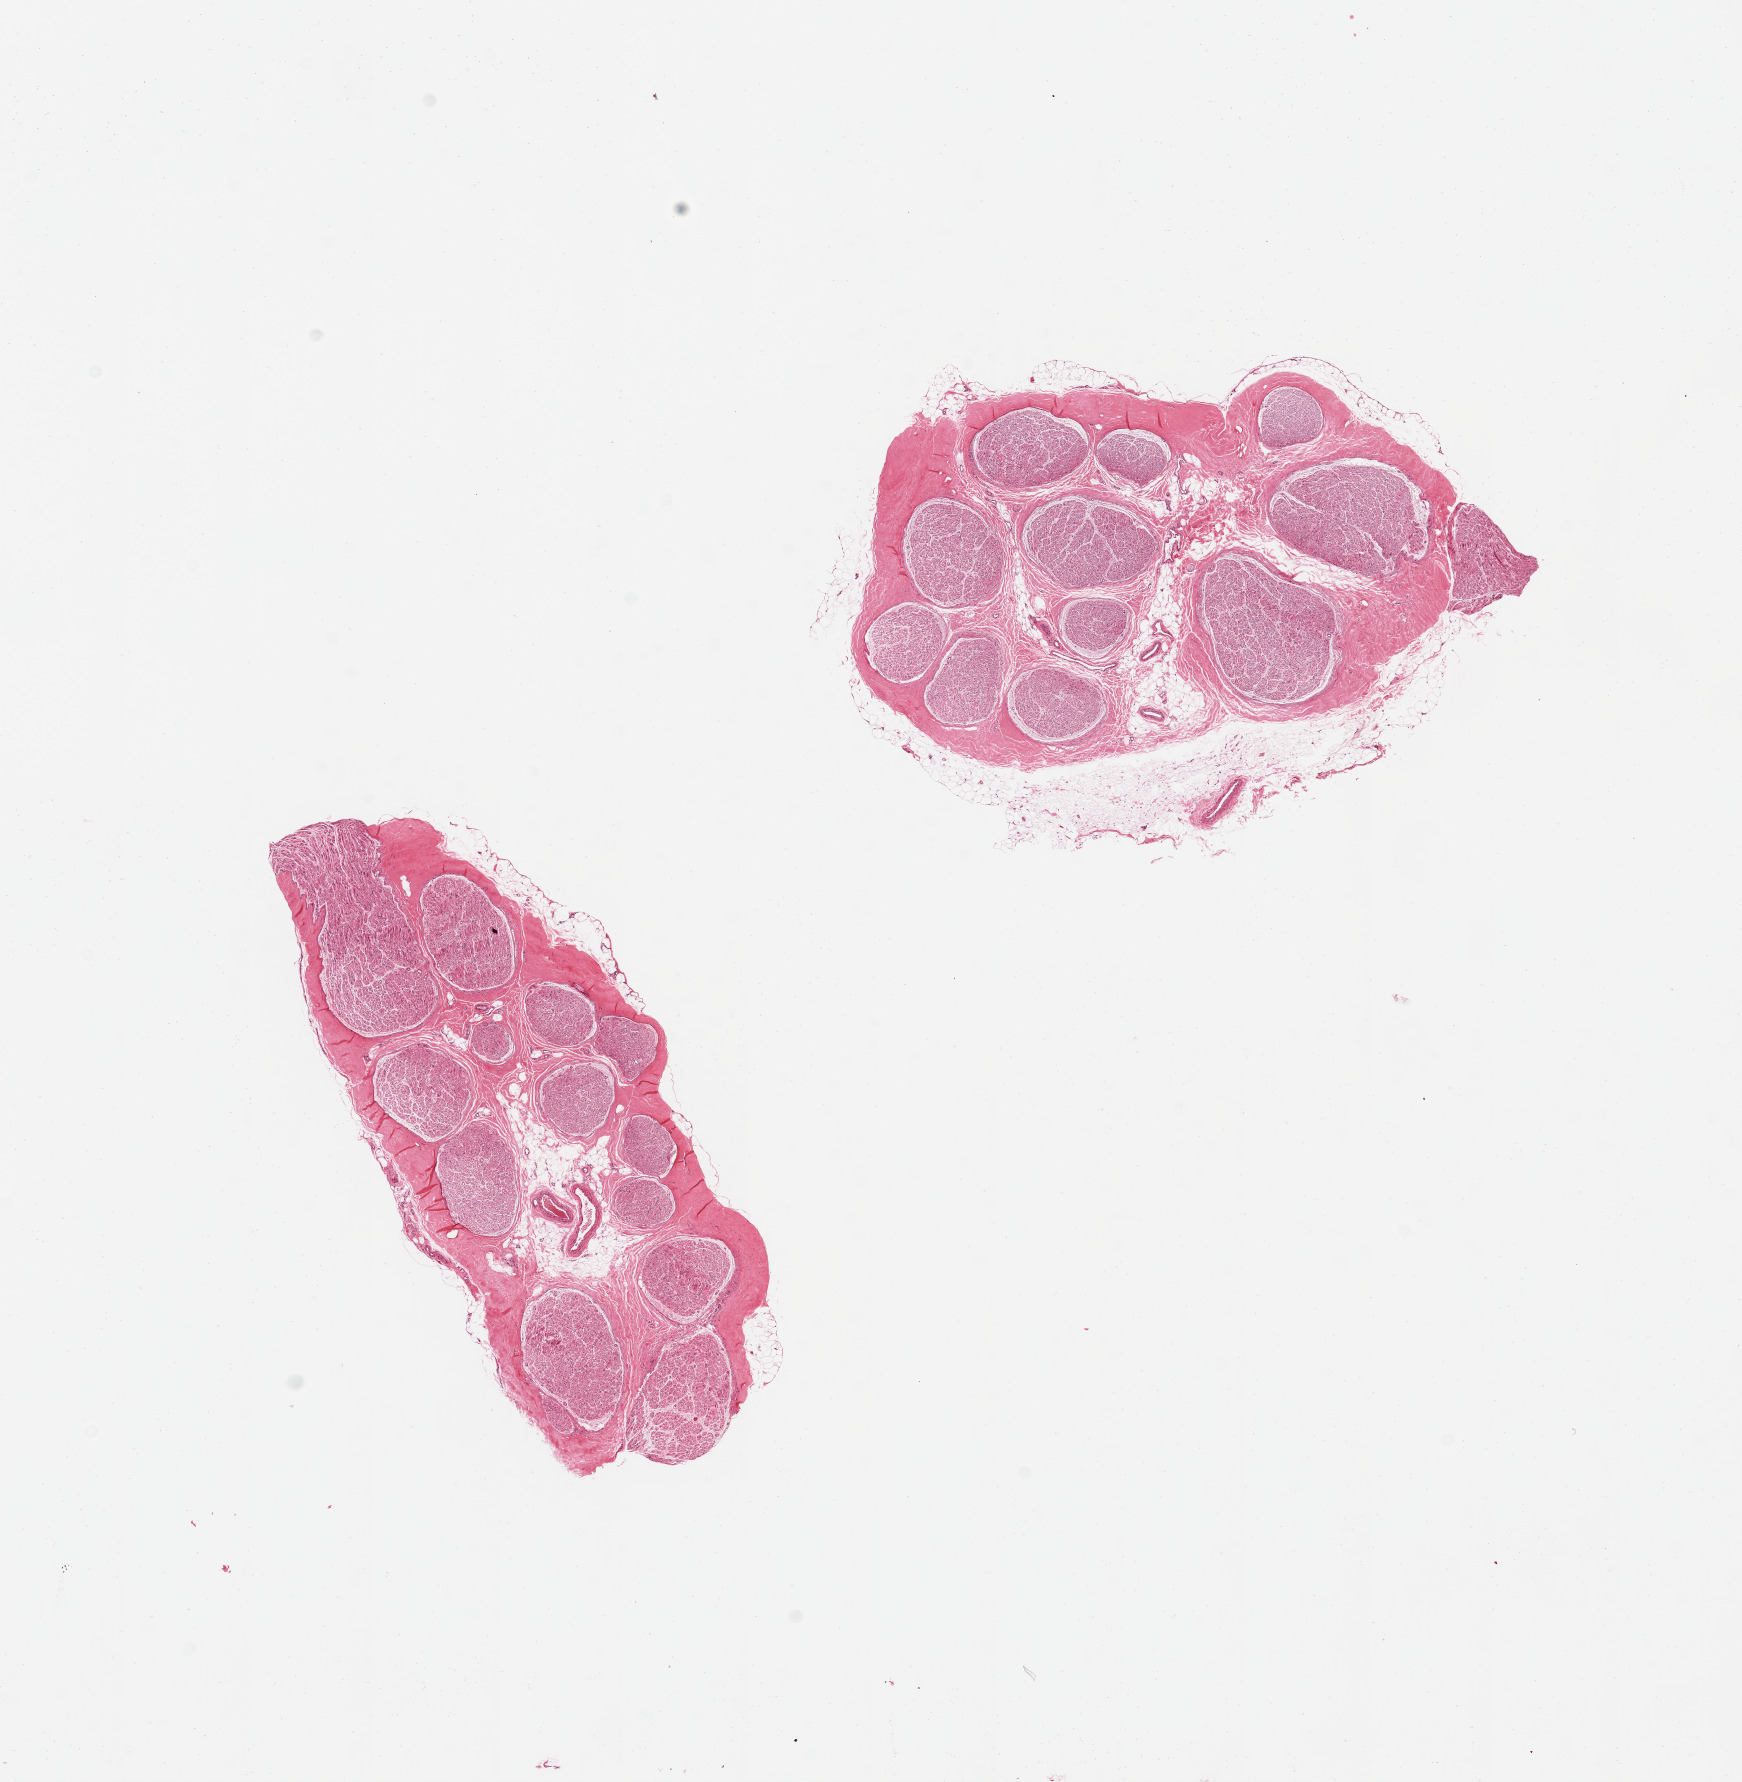
Whole-slide image, hematoxylin and eosin (H&E) stain — low-resolution overview of the scanned area, about 13.8 x 14.1 mm (acquisition: 20x scan). PAXgene-fixed, paraffin-embedded tissue. Target tissue: tibial nerve. Donor tissue sample. Donor: male.
- pathologist's review note for this sample: 2 pieces, clean specimens, focal adherent nubbin of fat ~0.5mm